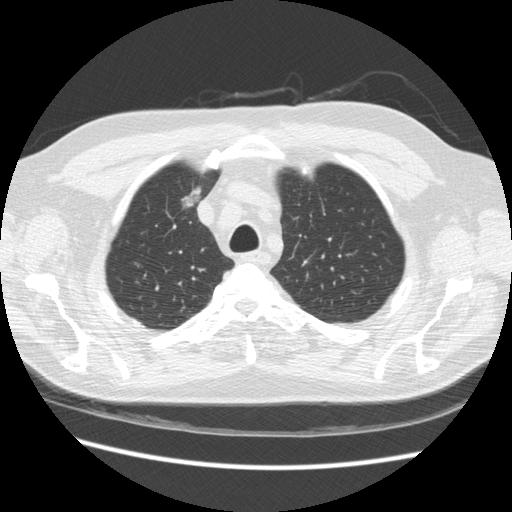
Axial slice from a low-dose chest CT screening exam. Third screening round (two years after baseline). Lung window (W 1500 / L -600 HU). Slice 49 of 234 in the series. 512 × 512 image matrix, field of view 360 × 360 mm. Male, age 66 years at enrolment.
• Lesion marked by an expert reader, bounding box [x1, y1, x2, y2] px = [165, 177, 212, 219].
• Screening reader's record for this exam: no non-calcified nodule ≥4 mm recorded.
• Participant outcome: lung cancer diagnosed 229 days after this screen — bronchiolo-alveolar adenocarcinoma, NOS, right upper lobe, moderately differentiated (G2), stage IA (AJCC 6th edition), 12 mm at pathology.